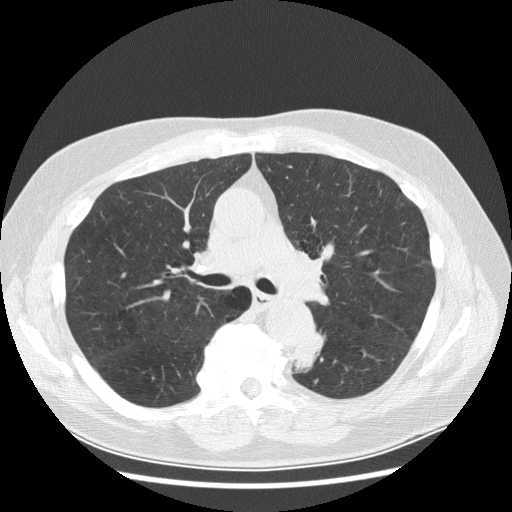
Low-dose screening chest CT, one axial slice. Lung window (W 1500 / L -600 HU). 2.5 mm slice thickness. 512 × 512 image matrix, field of view 370 × 370 mm.
Structures marked on this image (outlined manually by an expert reader):
- lesion 1 (tumor, lower lobe of left lung): box from (x=293, y=332) to (x=326, y=373) px